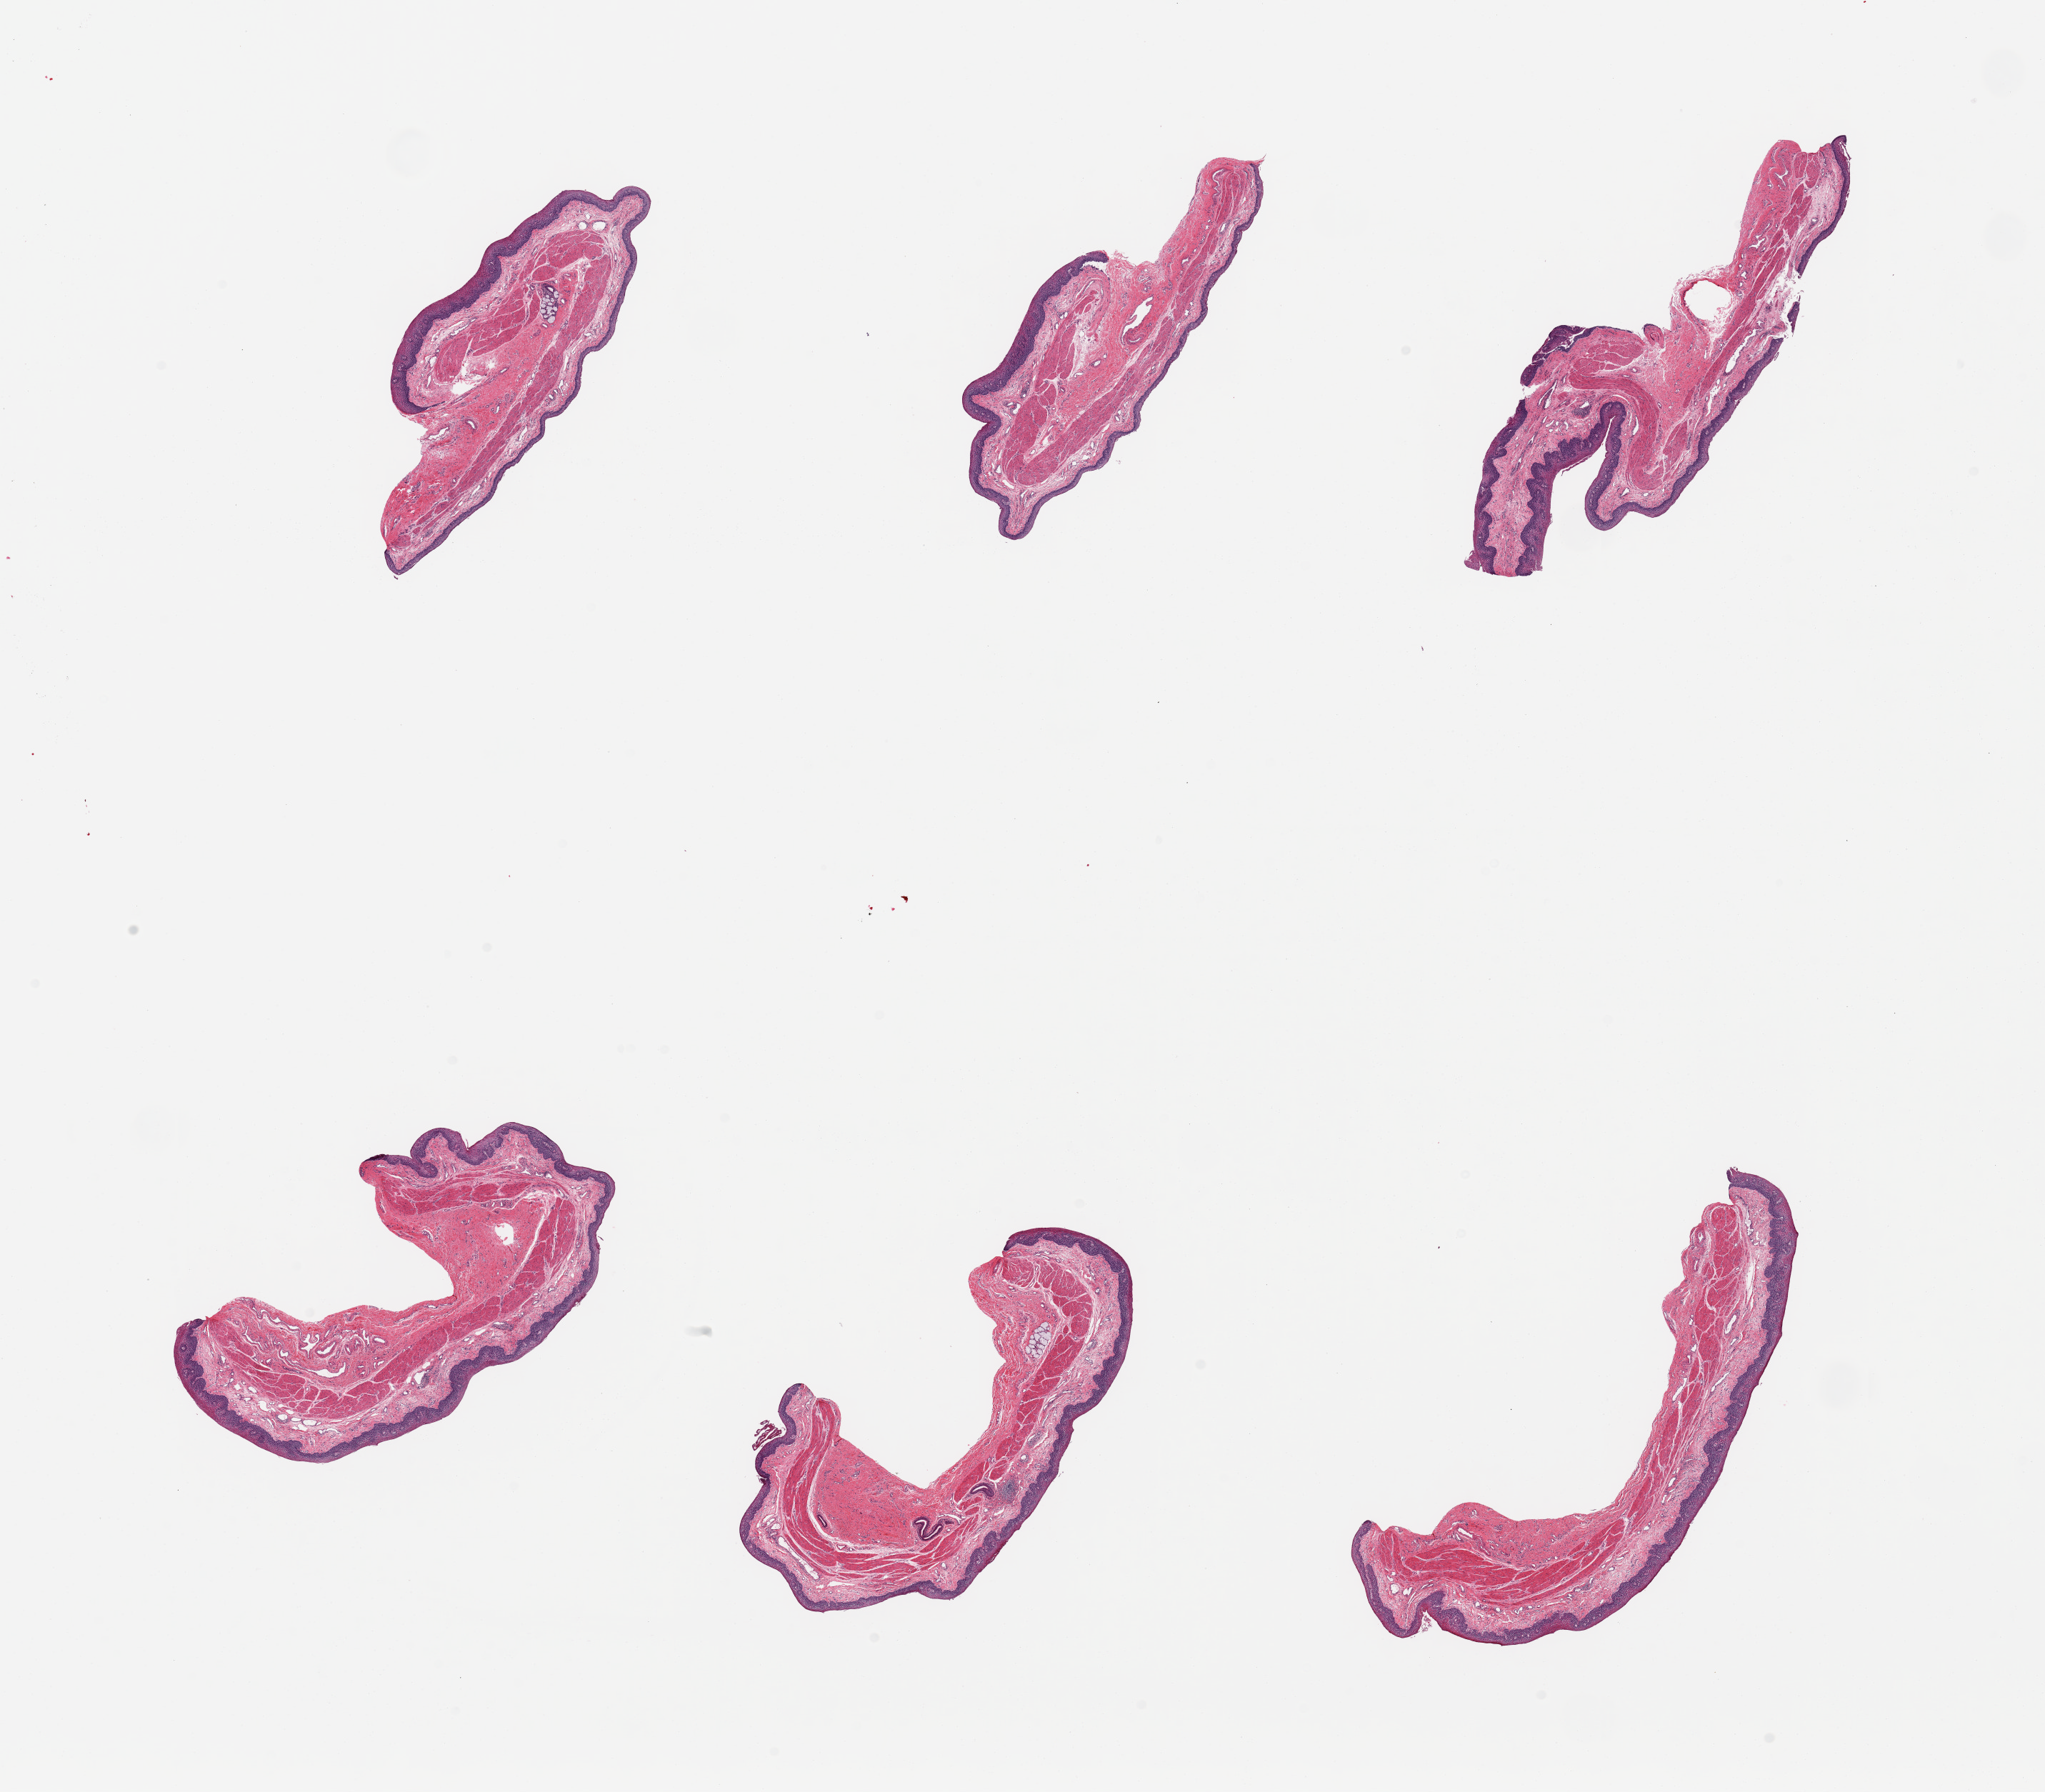
H&E whole-slide image, brightfield — a low-resolution overview of the entire scanned area, about 22.6 x 19.8 mm; PAXgene-fixed paraffin-embedded (PFPE) section; sampled site (target tissue): esophageal mucous membrane; tissue donor sample.
Review note (as recorded): 6 pieces; well dissected.